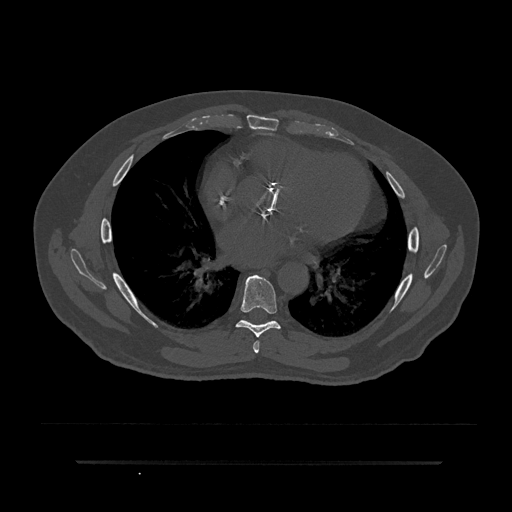
CT including the spine, one axial slice. 120 kVp. Bone window (W 1800 / L 400 HU). 0.5 mm slice thickness. 512 × 512 image matrix, field of view 464 × 464 mm. Patient: male, 59 years. Case-level facts recorded for this patient, not image findings: primary cancer: bile ducts; vertebrae with lytic lesions (as recorded): T10.
Annotated regions visible in this slice (semi-automatic segmentation, software-assisted and operator-edited):
- T6 vertebra: bounding box (x1, y1, x2, y2) in pixels: (253, 341, 260, 353)
- T7 vertebra: (235, 275, 281, 338)